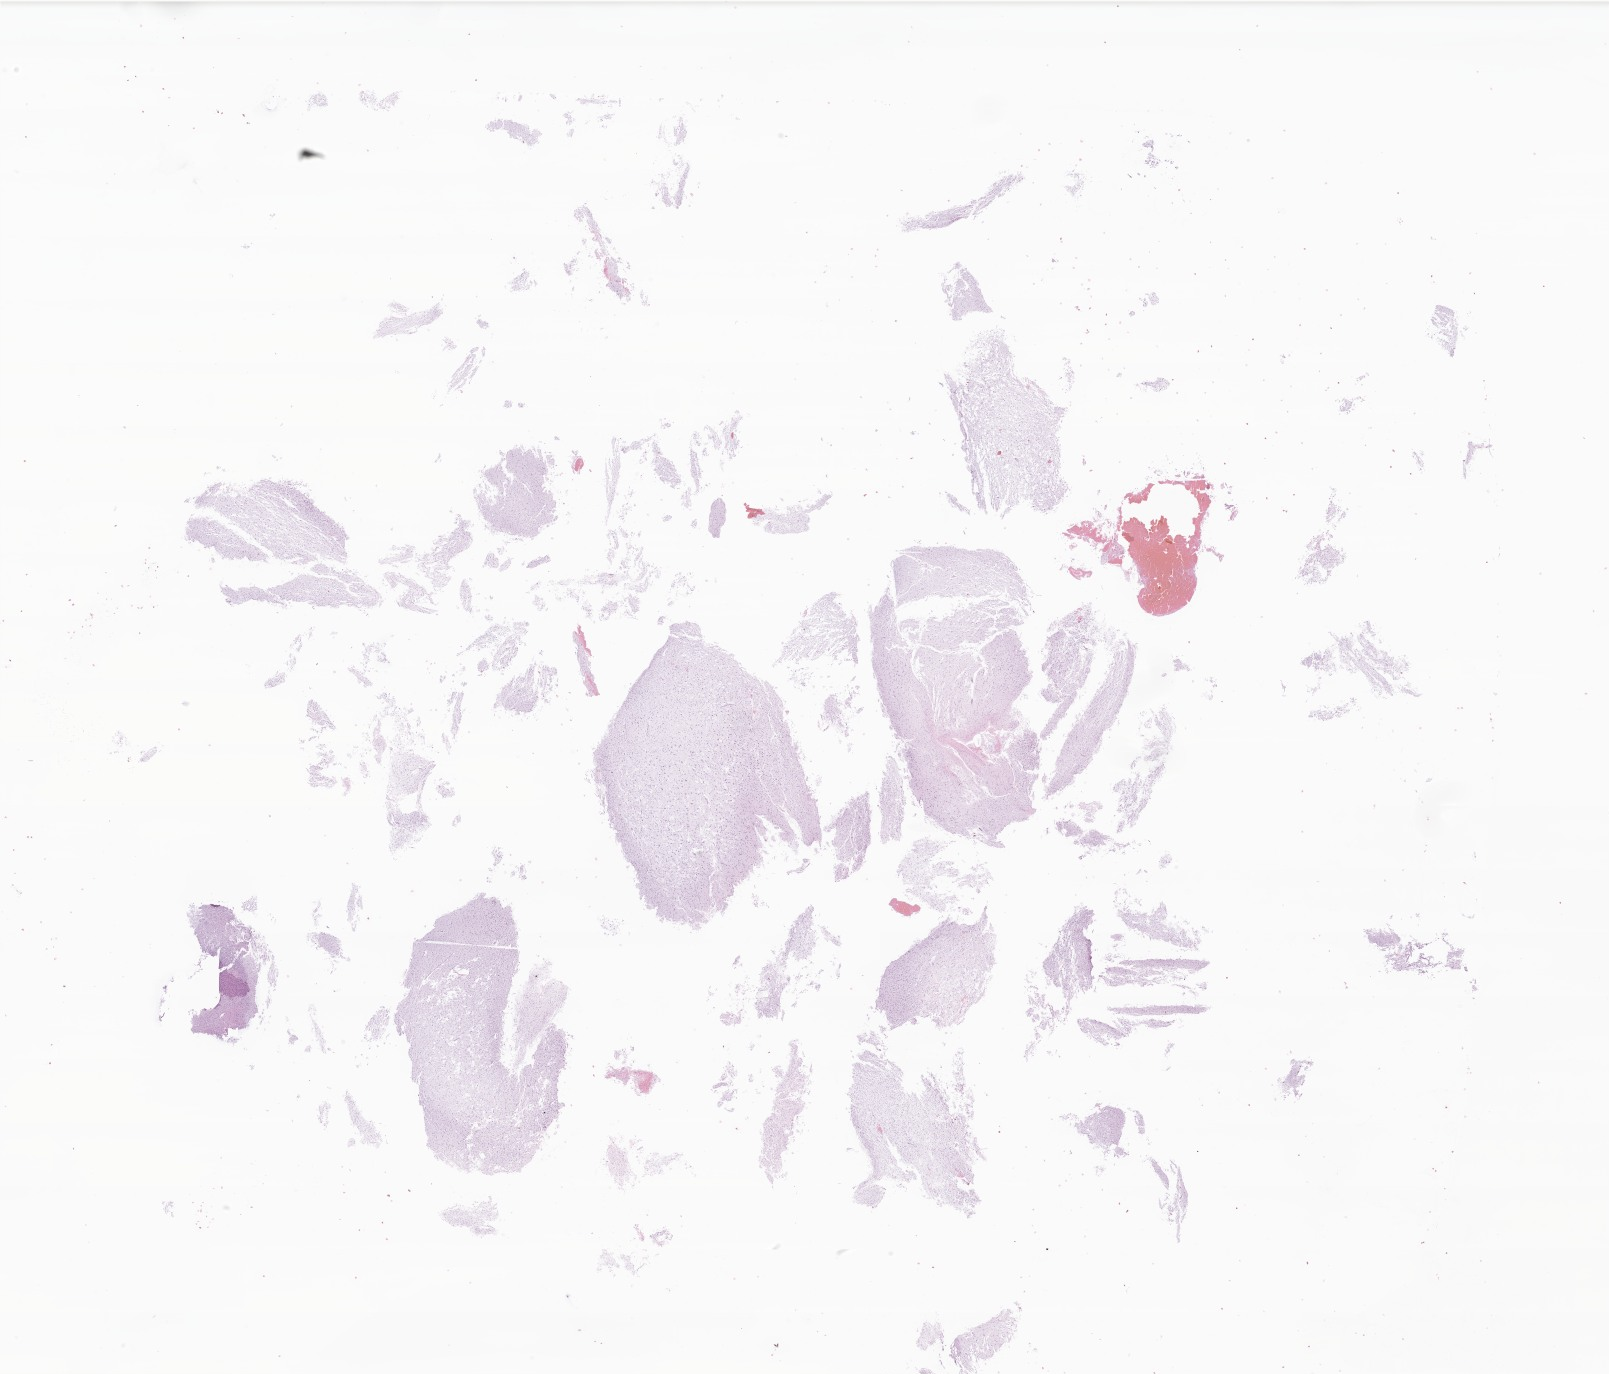
Digitized hematoxylin and eosin (H&E)-stained section of tumor tissue from the temporal lobe, a low-resolution overview of the entire scanned area, about 27.1 x 23.2 mm. Formalin-fixed paraffin-embedded section. Patient female; age 136 months (11 years 4 months).
* diagnosis (ICD-O-3 morphology term): Neoplasm, uncertain whether benign or malignant